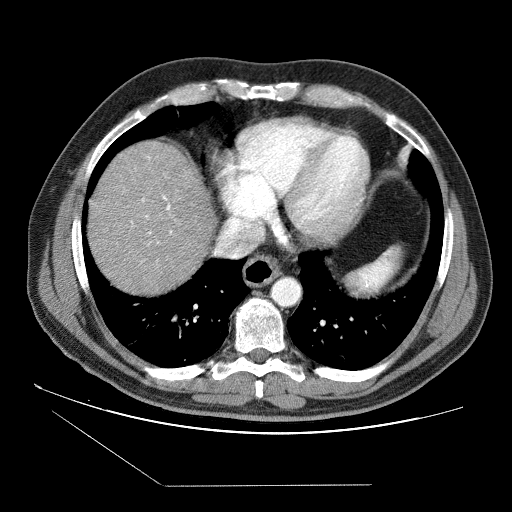
Contrast-enhanced abdominal CT (liver protocol), one axial slice; position 75 of 87 along the scan axis; reconstruction kernel STANDARD; 120 kVp; soft-tissue window (W 400 / L 40 HU); 512 × 512 image matrix. Case-level facts recorded for this patient, not image findings: diagnosis: hepatocellular carcinoma (patient treated with transarterial chemoembolisation; whether this scan precedes or follows treatment is not stated here); TNM stage (as recorded): Stage-II; Child-Pugh class: B; tumour nodularity: multinodular.
Structures marked on this image (semi-automatically segmented with operator editing):
- liver parenchyma outside the tumour (the mass and vessels are separate outlines, so this box may not span the whole liver): bounding box [x1, y1, x2, y2] px = [88, 140, 214, 294]
- liver vessels: [131, 157, 172, 245]